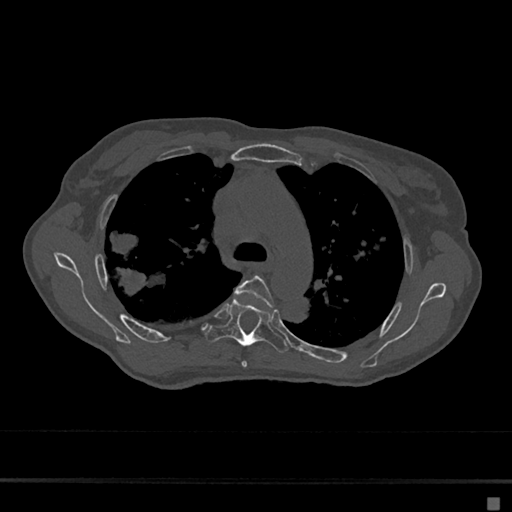
CT including the spine, one axial slice. Slice 474 of 797 in the series (ordered by position). Bone window (W 1800 / L 400 HU). 0.5 mm slice thickness. 512 × 512 image matrix, field of view 360 × 360 mm. Patient: female, 68 years. From the clinical record (not read from this slice): primary cancer: renal.
Structures marked on this image (semi-automatically segmented with operator editing):
- T4 vertebra: bounding box (x1, y1, x2, y2) in pixels: (235, 275, 275, 367)
- T5 vertebra: (206, 299, 289, 352)